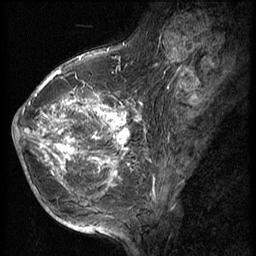
Breast MRI (dynamic contrast-enhanced), one sagittal slice. Slice 22 of 56 in the series (ordered by position). 3 images stored at this slice position (order not interpretable as contrast timing). 1.5 T. TE 4.2 ms, TR 9 ms. 2.5 mm slice thickness. 256 × 256 image matrix, field of view 180 × 180 mm. Female patient, age 49 years. From the clinical record (not read from this slice): setting: breast cancer imaged before/during neoadjuvant chemotherapy; receptor status: HER2-positive.
Annotated regions visible in this slice (semi-automatic segmentation, software-assisted and operator-edited):
- analysis volume of interest (the breast-tissue region the enhancement analysis was run in; not a lesion): box from (x=13, y=79) to (x=135, y=203) px
- tumour enhancement mask (voxels above the 140 % enhancement threshold inside the analysis volume of interest): (x=15, y=79)–(x=132, y=194)